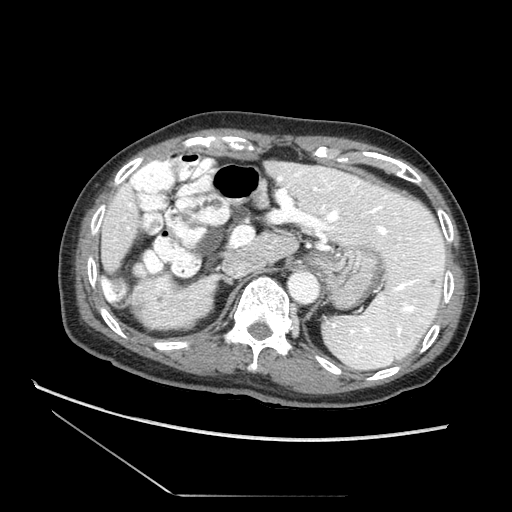
Contrast-enhanced abdominal CT (liver protocol), one axial slice. Slice 52 of 73 in the series (ordered by position). Reconstruction kernel STANDARD. Soft-tissue window (W 400 / L 40 HU). 2.5 mm slice thickness. 512 × 512 image matrix. From the clinical record (not read from this slice): diagnosis: hepatocellular carcinoma (patient treated with transarterial chemoembolisation; whether this scan precedes or follows treatment is not stated here); TNM stage (as recorded): Stage-II; Child-Pugh class: A.
Structures marked on this image (semi-automatic segmentation, software-assisted and operator-edited):
- liver parenchyma outside the tumour (the mass and vessels are separate outlines, so this box may not span the whole liver): bounding box <102,161,446,363> (left, top, right, bottom; pixels)
- liver vessels: <313,186,427,280>